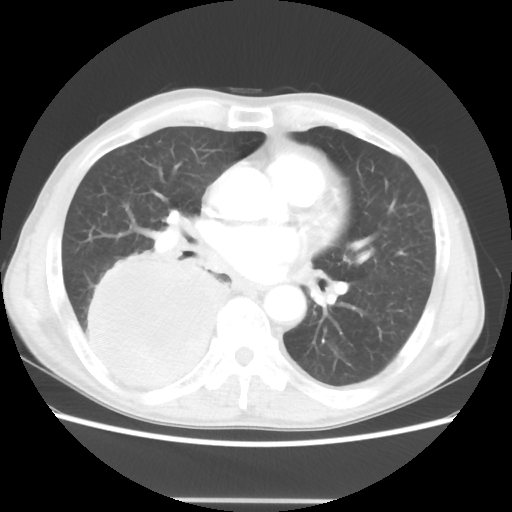
Chest CT, one axial slice. Position 22 of 48 along the scan axis. Reconstruction kernel STANDARD. Lung window (W 1500 / L -600 HU). 5 mm slice thickness. 512 × 512 image matrix. Patient: male, 66 years. From the clinical record (not read from this slice): clinical TNM (as recorded): T4 N1 M1; histopathological grade: G3.
Outlined on this slice (bounding box drawn by a radiologist):
- lung tumour (recorded histology: small cell carcinoma): box from (x=82, y=253) to (x=238, y=402) px